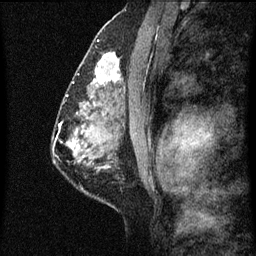
Breast MRI (dynamic contrast-enhanced), one sagittal slice. Slice 39 of 60 in the series (ordered by position). Dynamic contrast-enhanced series, image 2 of 7 at this slice position (ordered by acquisition). 1.5 T. TE 4.2 ms, TR 8 ms. 2 mm slice thickness. 256 × 256 image matrix, field of view 180 × 180 mm. Female patient, age 51 years.
Annotated regions visible in this slice (semi-automatic segmentation, software-assisted and operator-edited):
- analysis volume of interest (the breast-tissue region the enhancement analysis was run in; not a lesion): bounding box [x1, y1, x2, y2] px = [86, 50, 125, 101]
- tumour enhancement mask (voxels above the 70 % enhancement threshold inside the analysis volume of interest): [94, 54, 121, 87]